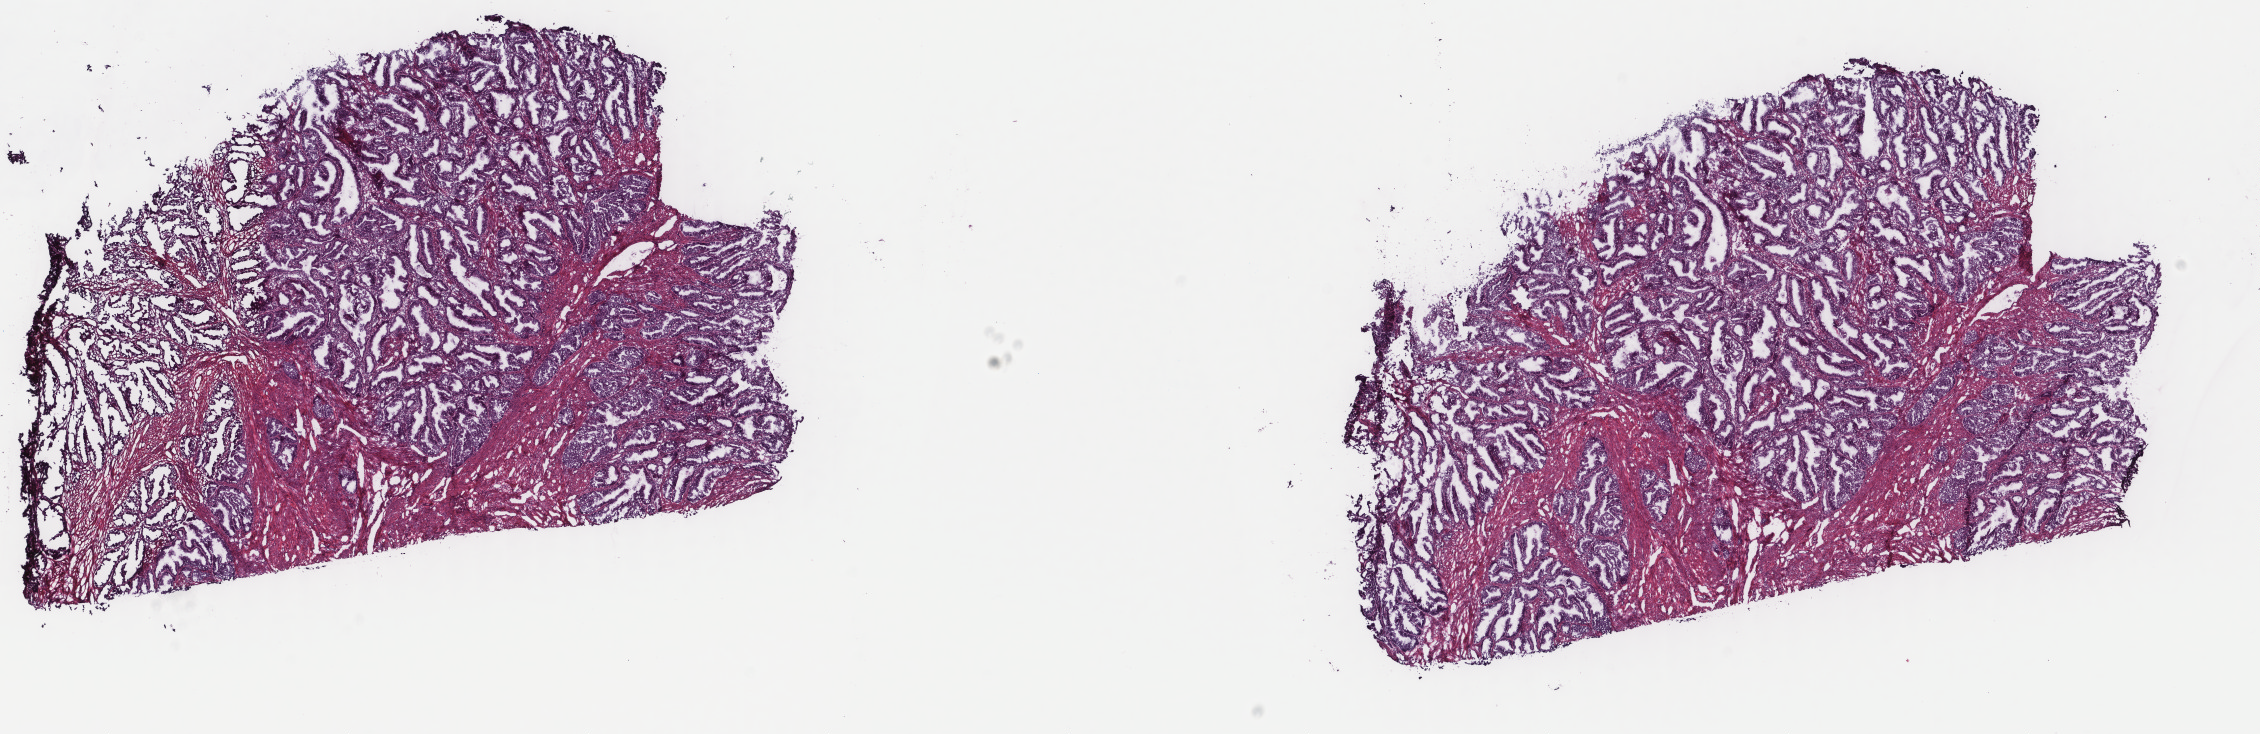
Whole-slide histology image, Hematoxylin and eosin (H&E) stained — a low-resolution overview of the entire scanned area, about 17.9 x 5.8 mm (acquisition: 40x scan); frozen section from the top of the tissue portion; primary tumour sample from the uterus. Female patient; age at initial diagnosis 78 years. Histologic grade: G1 (well differentiated). Pathologist review of this section (percent, as recorded): tumour cells 75%, tumour nuclei 60%, normal cells 25%, stromal cells 0%, necrosis 0%. Inflammatory infiltration, as recorded: lymphocyte infiltration 0%, monocyte infiltration 0%, neutrophil infiltration 0%.
FIGO stage: IC. Diagnosis: Endometrioid adenocarcinoma, NOS (endometrium).